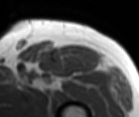
MRI of an extremity soft-tissue mass, one axial slice. Position 79 of 86 along the scan axis. MR volume resampled by the dataset authors to the PET/CT grid (not the native acquisition matrix). 139 × 117 image matrix, field of view 136 × 114 mm. Male patient. Case-level facts recorded for this patient, not image findings: histological type: extraskeletal osteosarcoma; grade: high; site of the primary tumour: thigh.
Annotated regions visible in this slice (expert contour drawn on MRI and transferred to this co-registered scan by the dataset authors):
- gross tumour volume (mass): bounding box [x1, y1, x2, y2] px = [61, 45, 101, 65]